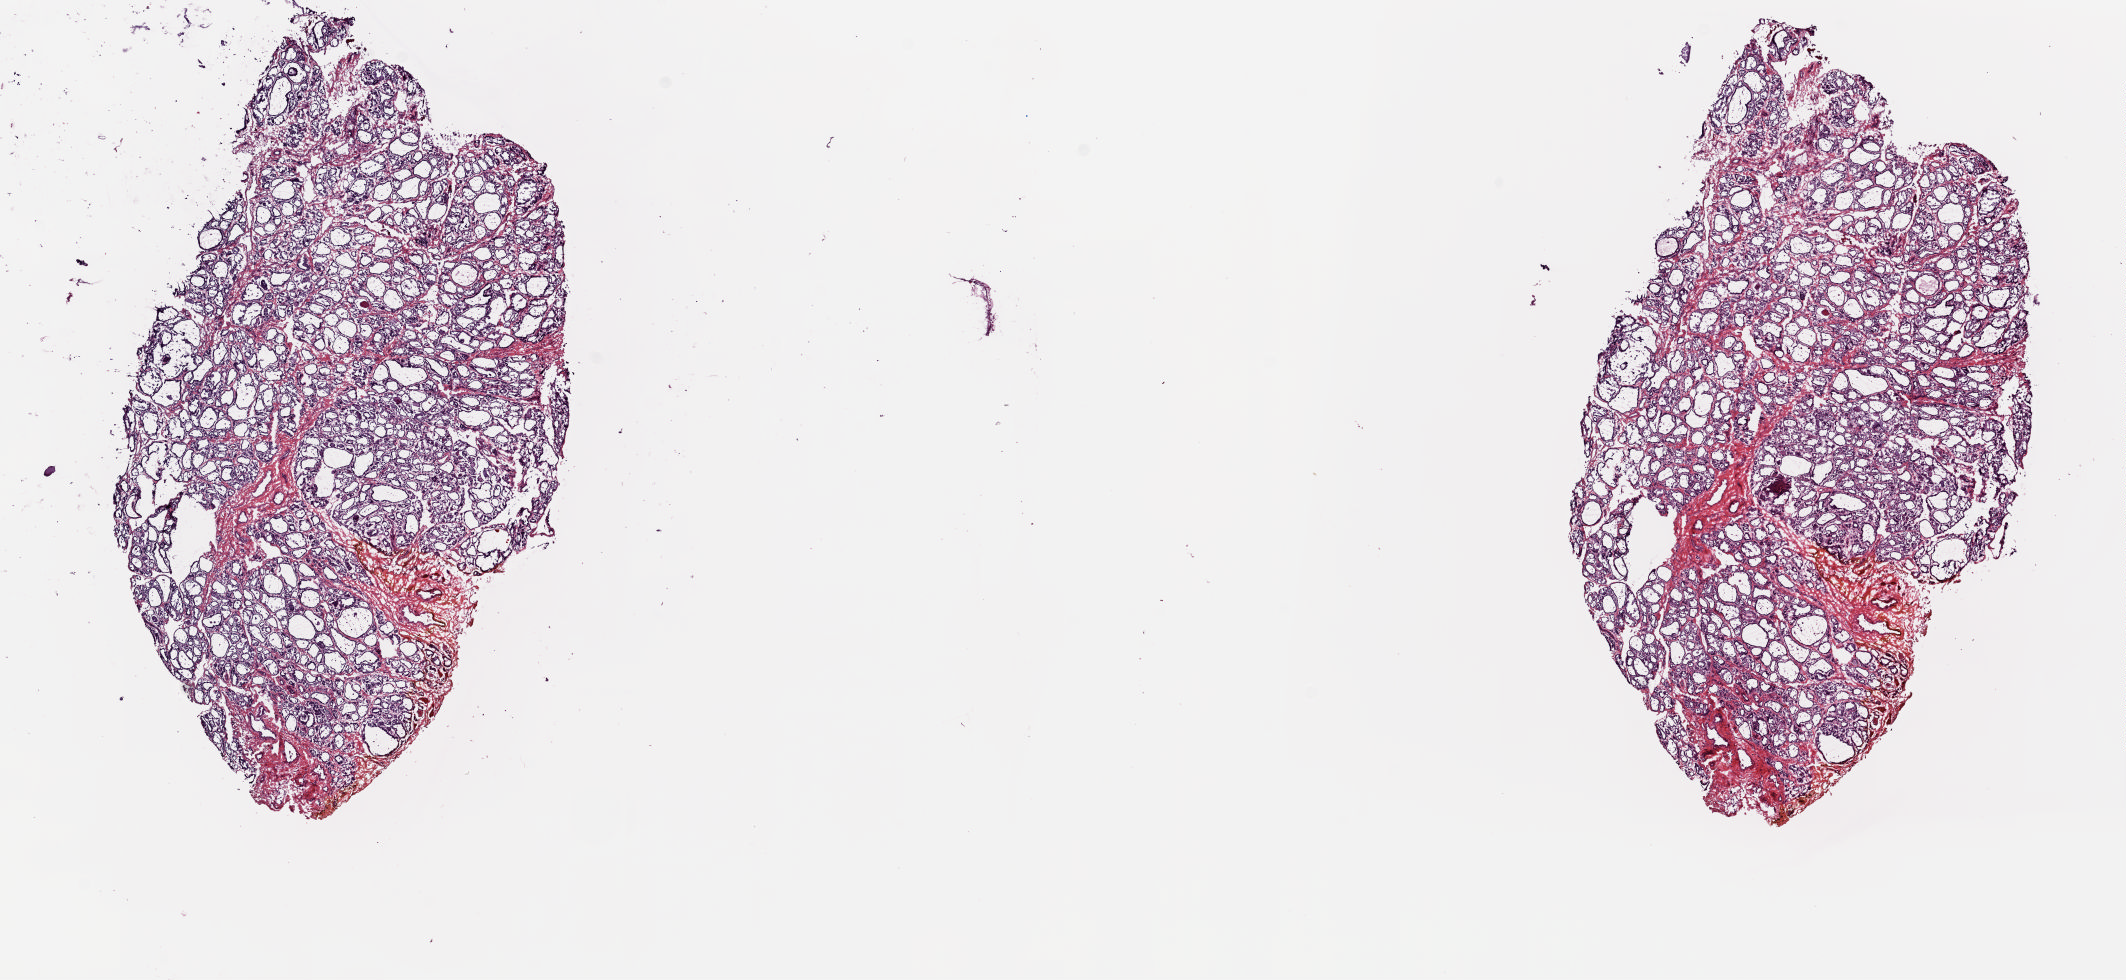
H&E-stained whole-slide image, low-resolution overview of the scanned area, about 16.9 x 7.8 mm, frozen section from the top of the tissue portion, sample: solid tissue normal (non-tumour tissue), thyroid. Female, age 62 years at initial diagnosis. Pathologist review of this section (percent, as recorded): tumour cells 0%, tumour nuclei 0%.
This section: solid tissue normal (non-tumour) sample from the same patient. Patient diagnosis: Papillary carcinoma, follicular variant (thyroid gland).